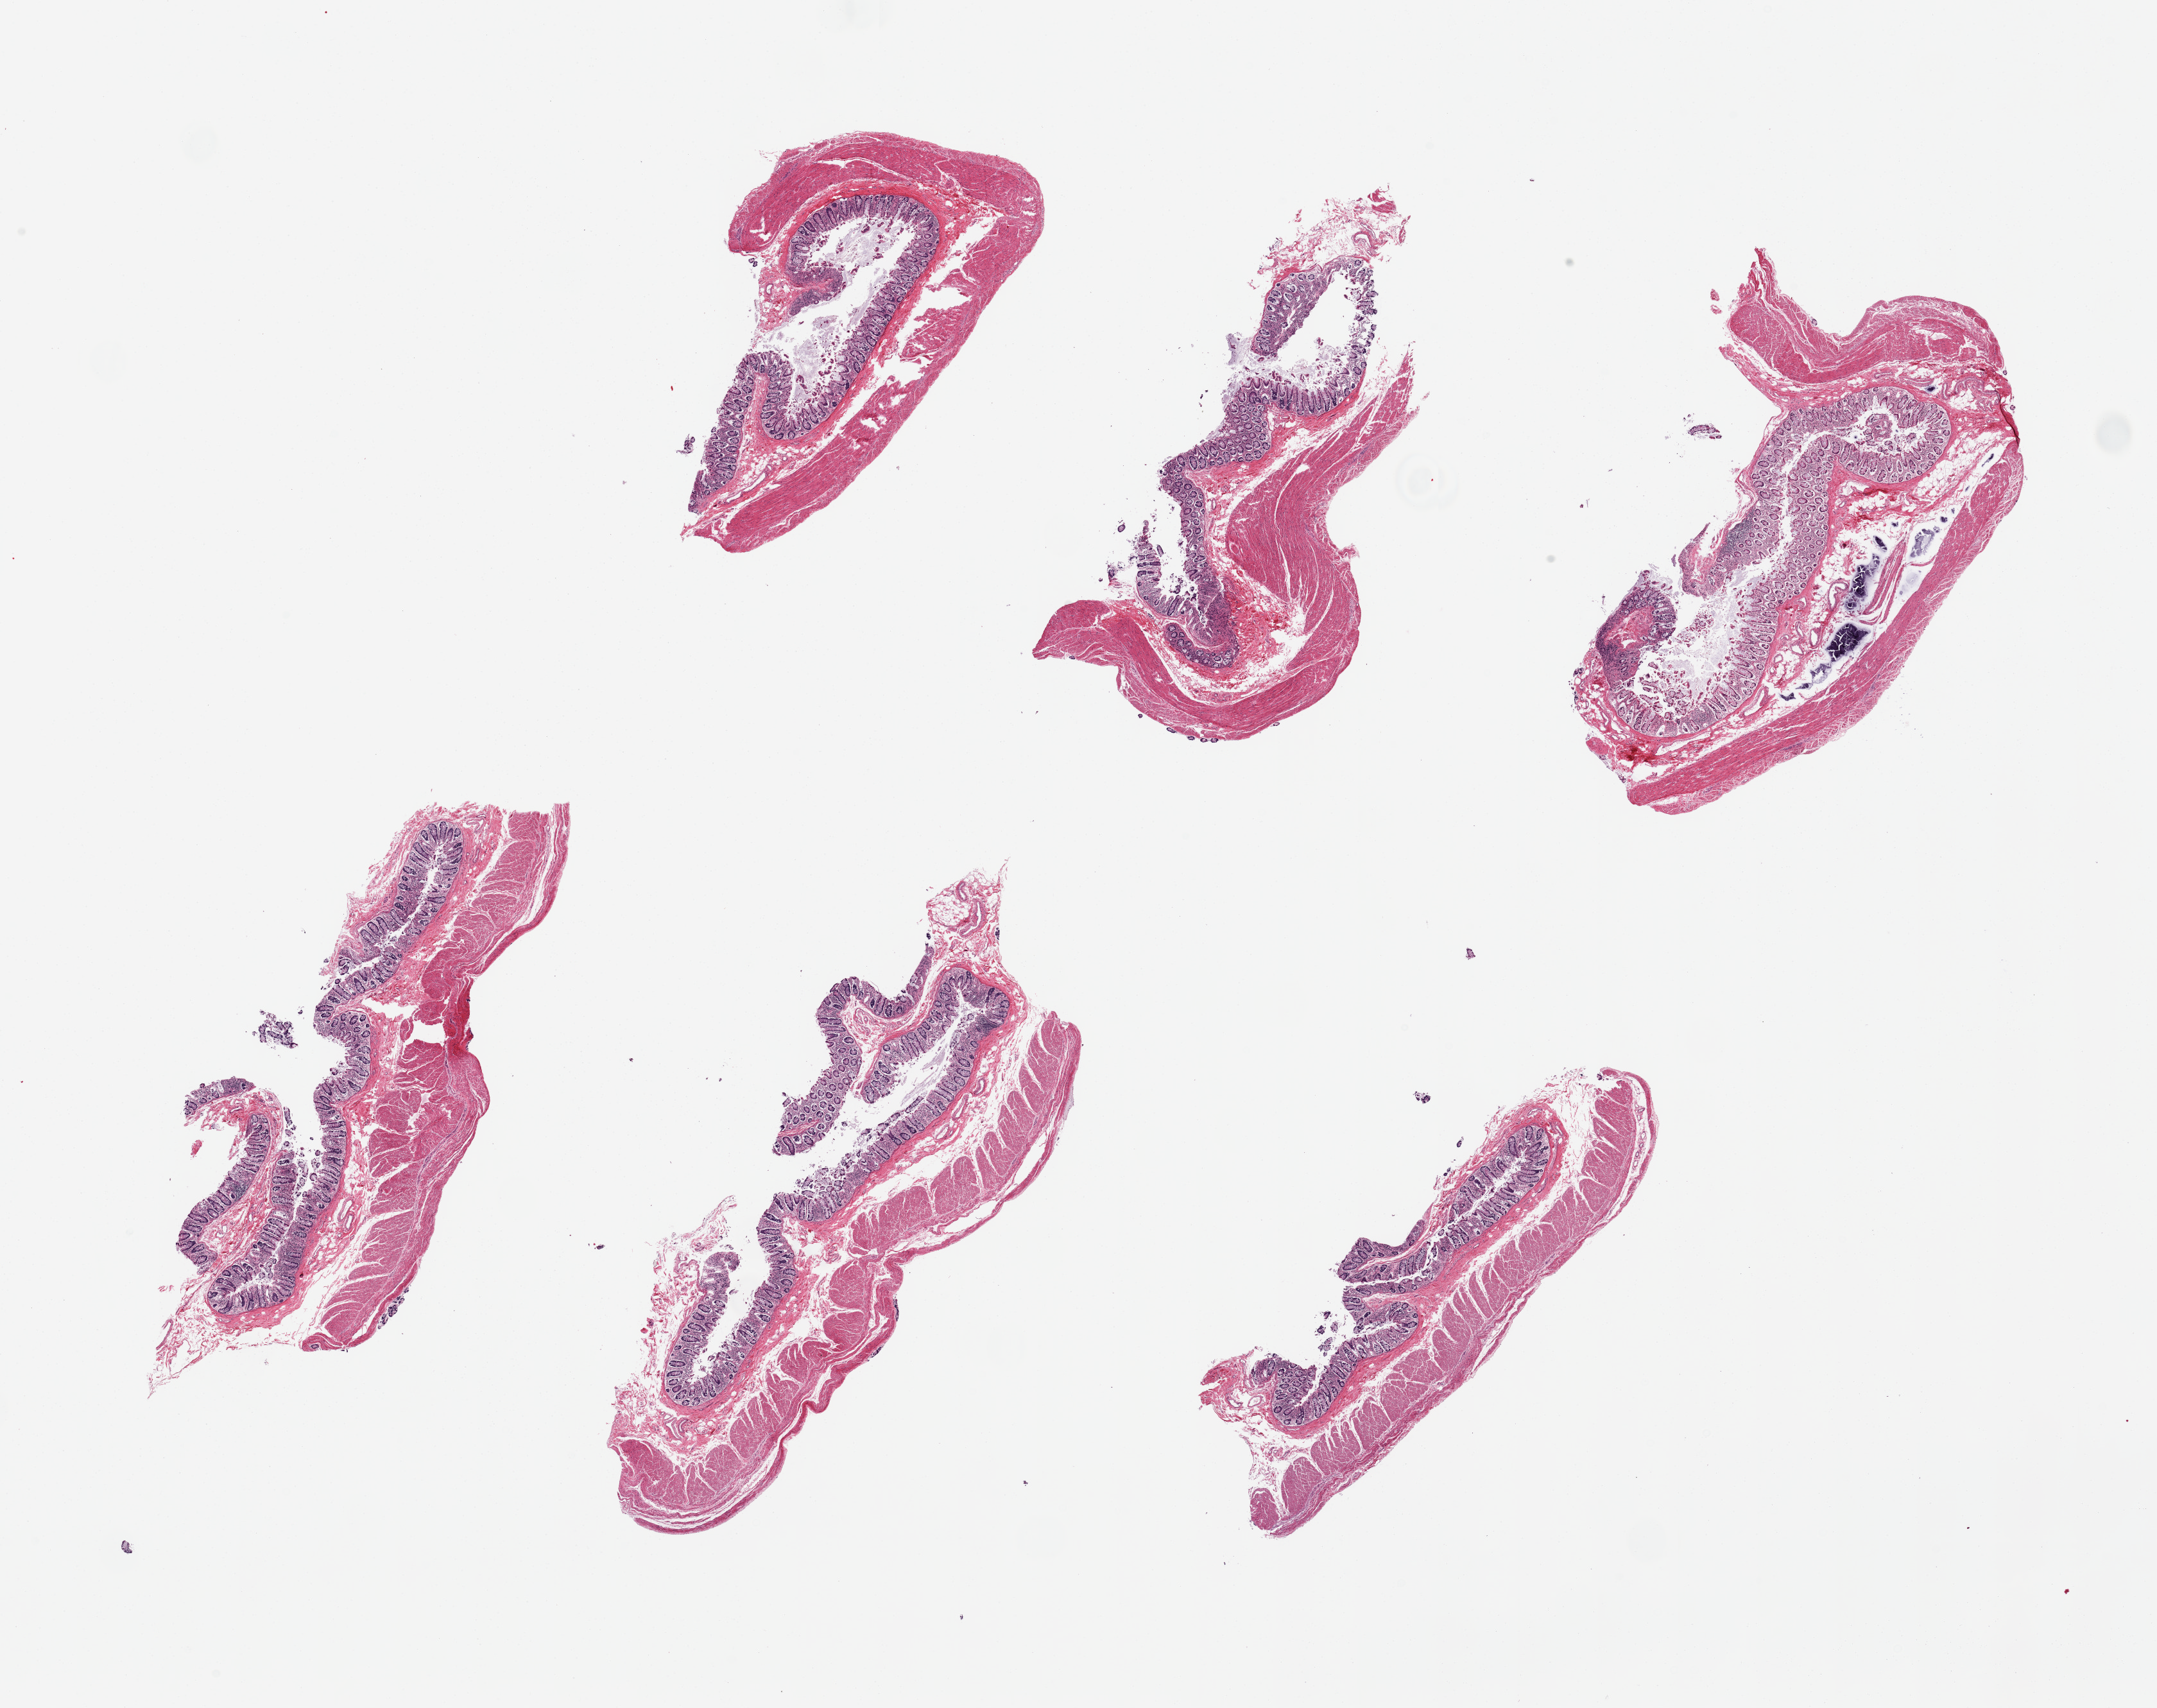
Whole-slide image, haematoxylin and eosin stain — a low-resolution overview of the entire scanned area, about 26.6 x 21.0 mm (from a 20x scan); PAXgene-fixed paraffin-embedded (PFPE) section; sampled site (target tissue): transverse colon; donor tissue sample. Donor: female.
• reviewer comment on this tissue sample: 6 pieces, Max 9x2mm. Tissue separation with tears